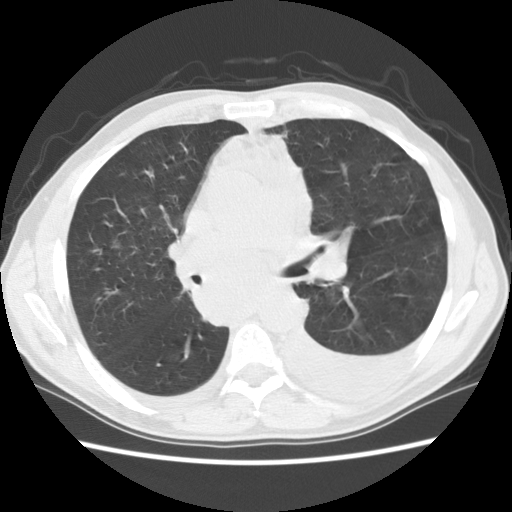
Axial slice from a low-dose chest CT screening exam. Baseline annual screen. Lung window (W 1500 / L -600 HU). Standard (soft-tissue) reconstruction kernel (STANDARD). Slice 51 of 135 in the series. Male, age 60 years at enrolment.
Expert reader's lesion annotation, bounding box (x1, y1, x2, y2) in pixels: (176, 238, 298, 329). No non-calcified nodule or mass ≥4 mm was recorded by the screening reader at this exam. Official screen result: negative screen, significant abnormalities not suspicious for lung cancer. Later outcome: lung cancer diagnosed 12 days after this screen — squamous cell carcinoma, NOS, carina, poorly differentiated (G3), stage IV (AJCC 6th edition).